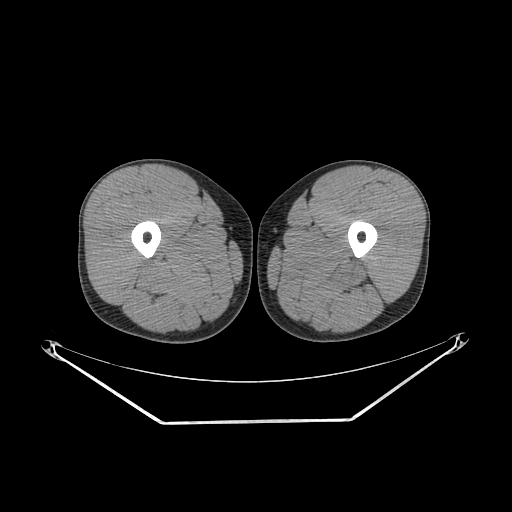
CT of an extremity soft-tissue mass (from a PET/CT study), one axial slice; slice 235 of 267 in the series (ordered by position); reconstruction kernel SOFT; soft-tissue window (W 400 / L 40 HU); 3.75 mm slice thickness; 512 × 512 image matrix, field of view 500 × 500 mm. Male patient. From the clinical record (not read from this slice): histological type: extraskeletal osteosarcoma; grade: high; site of the primary tumour: left adductur.
Annotated regions visible in this slice (expert contour drawn on MRI and transferred to this co-registered scan by the dataset authors):
- gross tumour volume (mass): bounding box (x1, y1, x2, y2) in pixels: (274, 244, 380, 296)